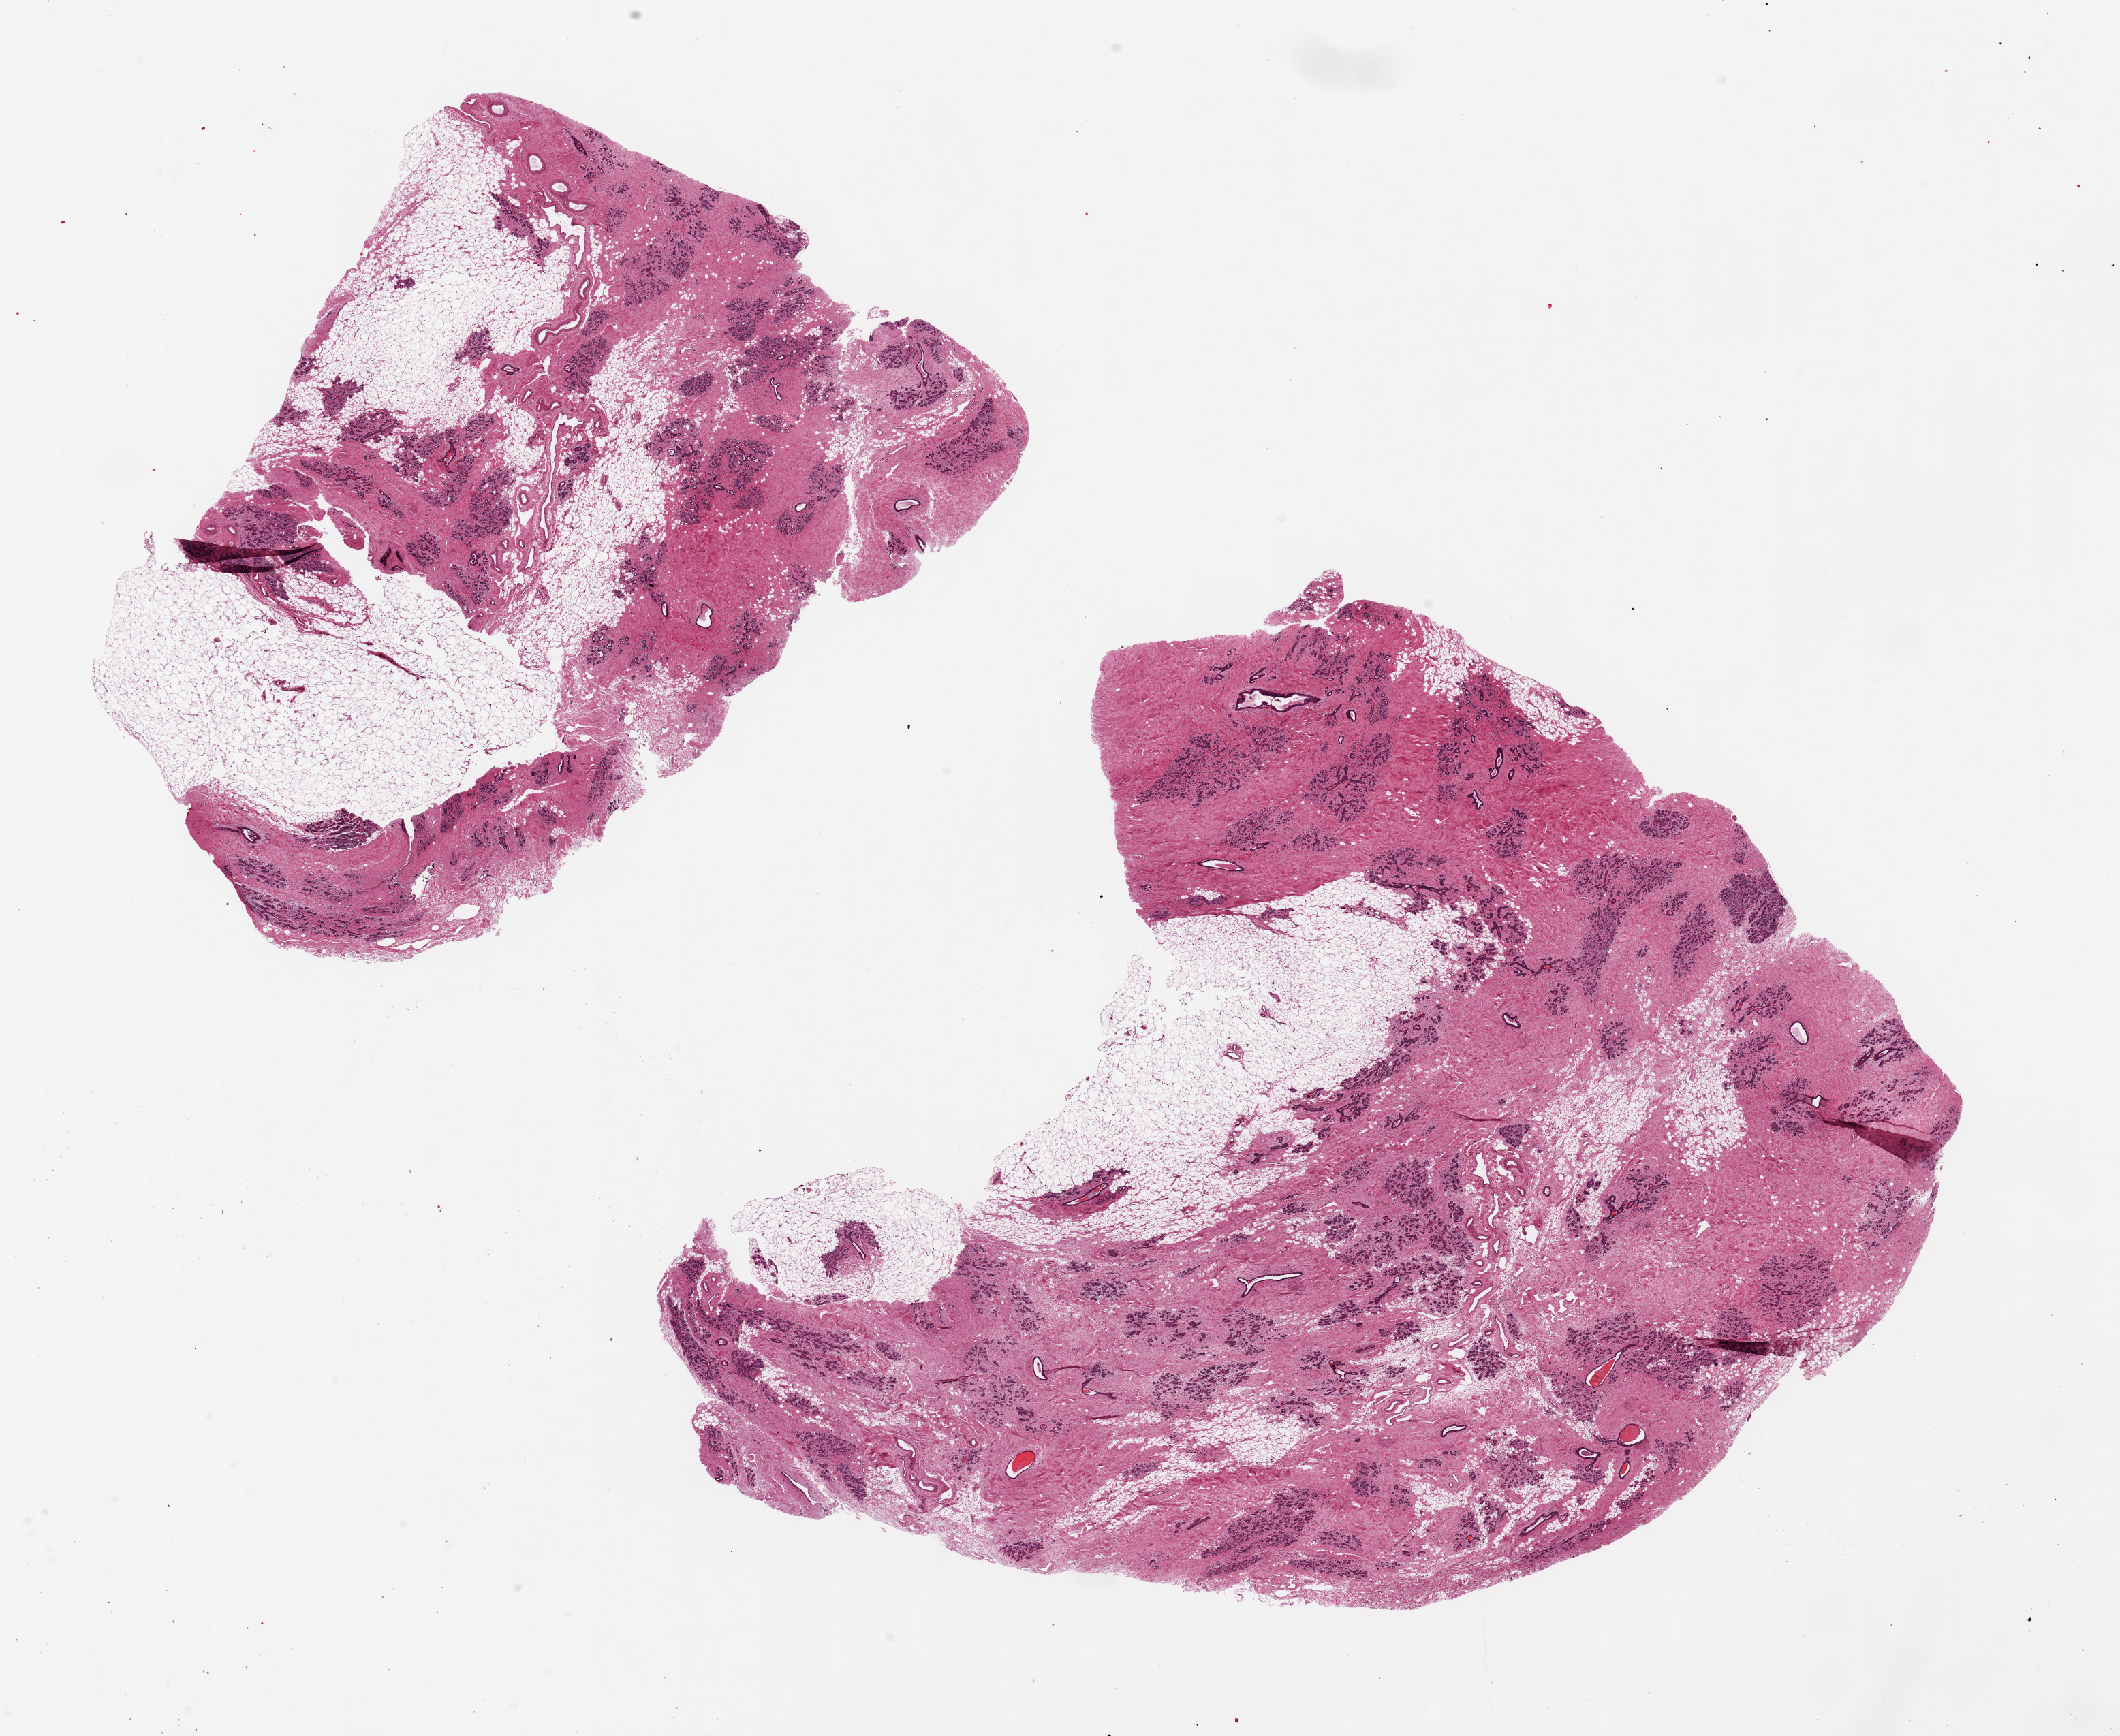
Digitized hematoxylin and eosin (H&E)-stained section, brightfield — low-resolution overview of the scanned area, about 24.6 x 20.2 mm. PAXgene-fixed, paraffin-embedded tissue. Target tissue: breast. Donor tissue sample.
- pathologist's review note for this sample: 2 pieces ~11x9mm, abundant TDLU's, post menopausal appearance